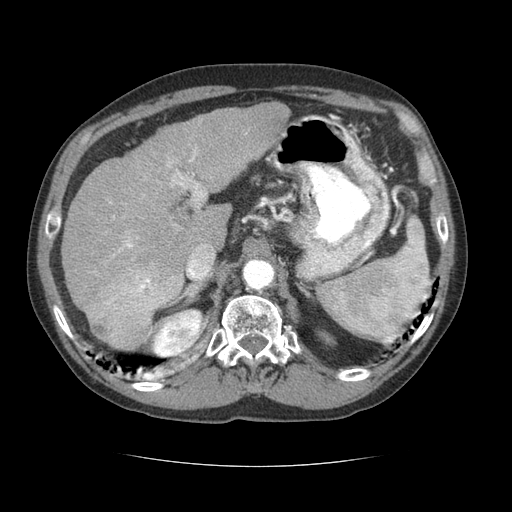
Contrast-enhanced abdominal CT (liver protocol), one axial slice; position 48 of 69 along the scan axis; 120 kVp; soft-tissue window (W 400 / L 40 HU); 512 × 512 image matrix. Case-level facts recorded for this patient, not image findings: diagnosis: hepatocellular carcinoma (patient treated with transarterial chemoembolisation; whether this scan precedes or follows treatment is not stated here); TNM stage (as recorded): Stage-II; Child-Pugh class: B; tumour size: 2.6 cm.
Structures marked on this image (semi-automatic segmentation, software-assisted and operator-edited):
- liver parenchyma outside the tumour (the mass and vessels are separate outlines, so this box may not span the whole liver): bounding box (x1, y1, x2, y2) in pixels: (62, 102, 290, 350)
- mass: (85, 263, 183, 349)
- liver vessels: (109, 149, 197, 304)